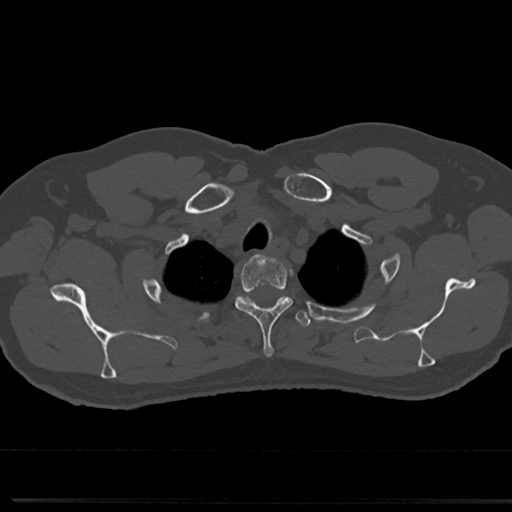
CT including the spine, one axial slice. Position 626 of 817 along the scan axis. Reconstruction kernel Br40s/3. Bone window (W 1800 / L 400 HU). 0.5 mm slice thickness. 512 × 512 image matrix. Patient: male, 61 years. Case-level facts recorded for this patient, not image findings: primary cancer: prostate.
Annotated regions visible in this slice (semi-automatic segmentation, software-assisted and operator-edited):
- T1 vertebra: box from (x=239, y=297) to (x=285, y=304) px
- T2 vertebra: (x=235, y=256)–(x=292, y=357)
- T3 vertebra: (x=219, y=297)–(x=312, y=329)